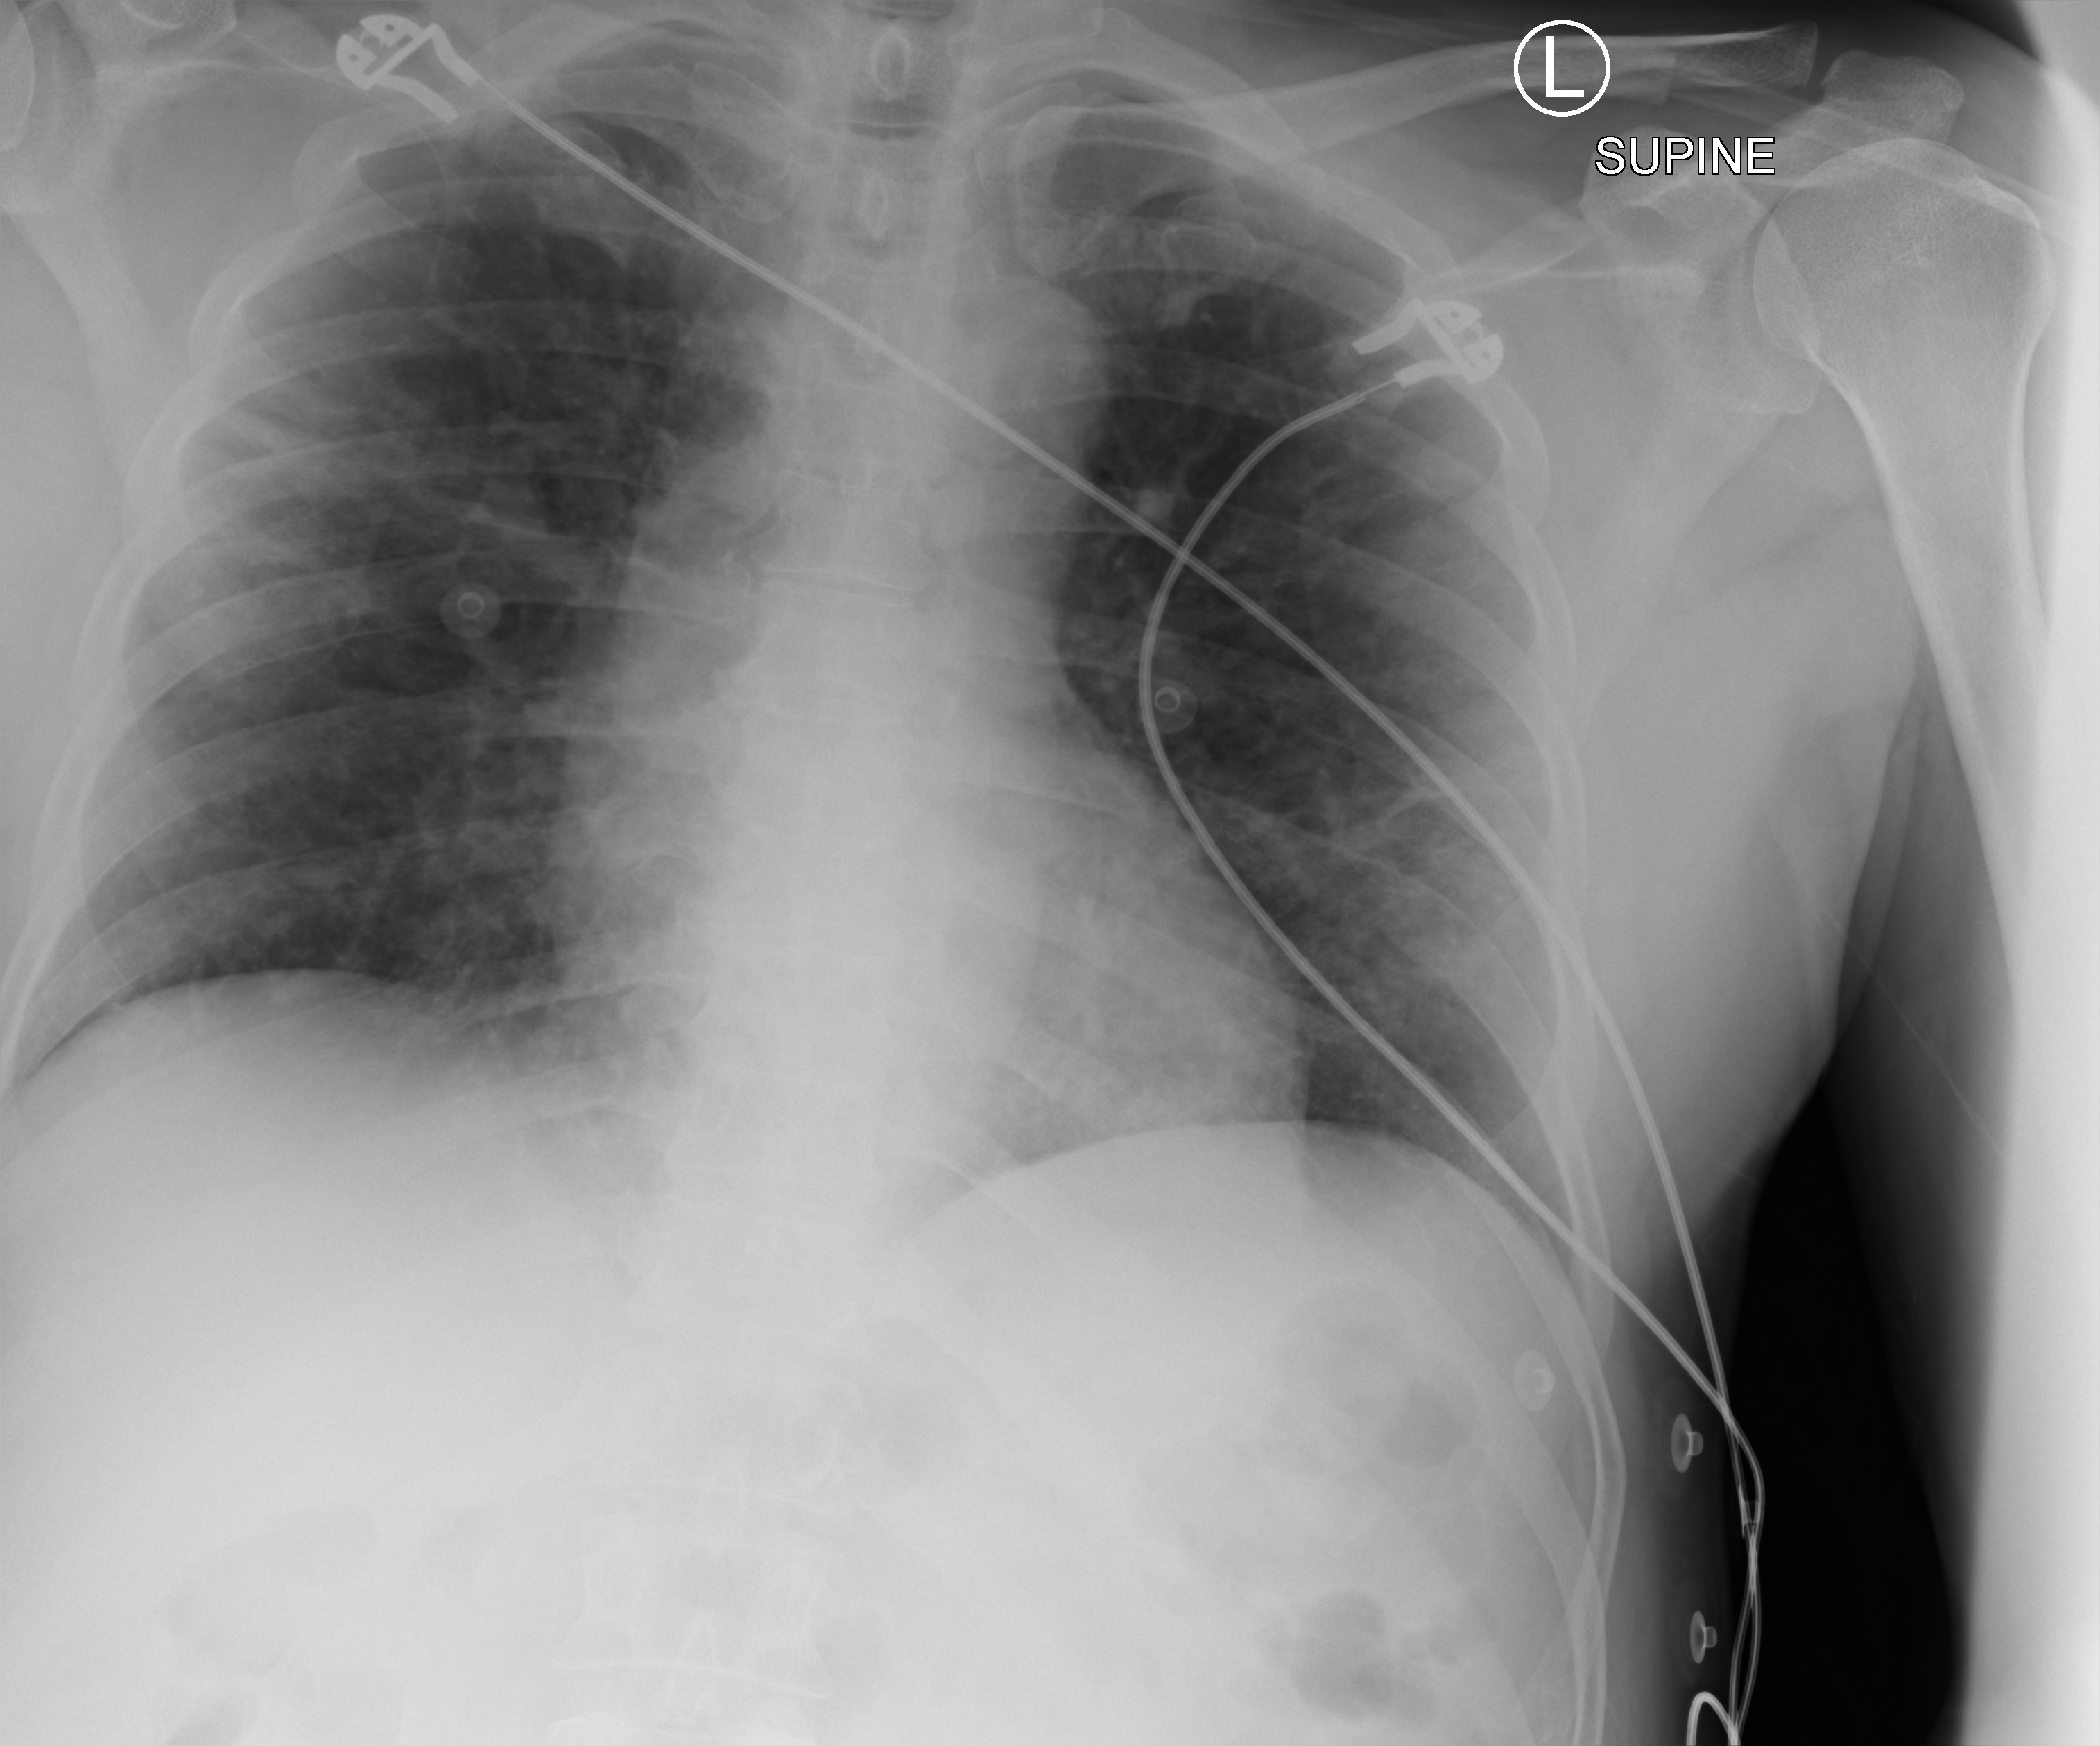
Chest X-ray (portable), anteroposterior (AP) projection. Male patient hospitalised with COVID-19, age 18–59 years.
Hospital-stay facts (about this admission, not read from this image; timing relative to this image not recorded):
- admitted to intensive care during this hospital stay: no
- diabetes (admission record): no